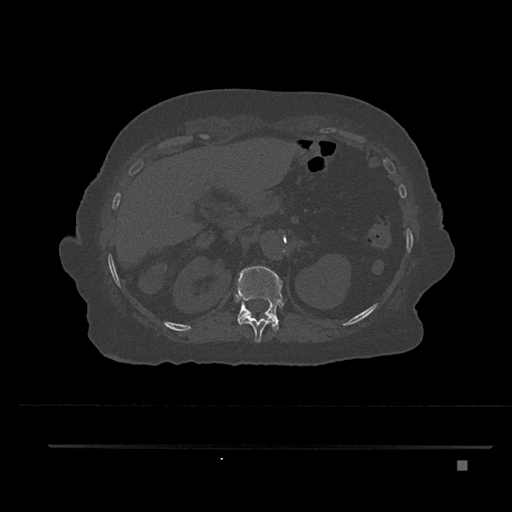
CT including the spine, one axial slice. Position 285 of 797 along the scan axis. 120 kVp. Bone window (W 1800 / L 400 HU). 0.5 mm slice thickness. 512 × 512 image matrix. Patient: female, 76 years. Case-level facts recorded for this patient, not image findings: primary cancer: lung.
Annotated regions visible in this slice (semi-automatic segmentation, software-assisted and operator-edited):
- T11 vertebra: bounding box (x1, y1, x2, y2) in pixels: (237, 282, 275, 343)
- T12 vertebra: (237, 266, 283, 331)